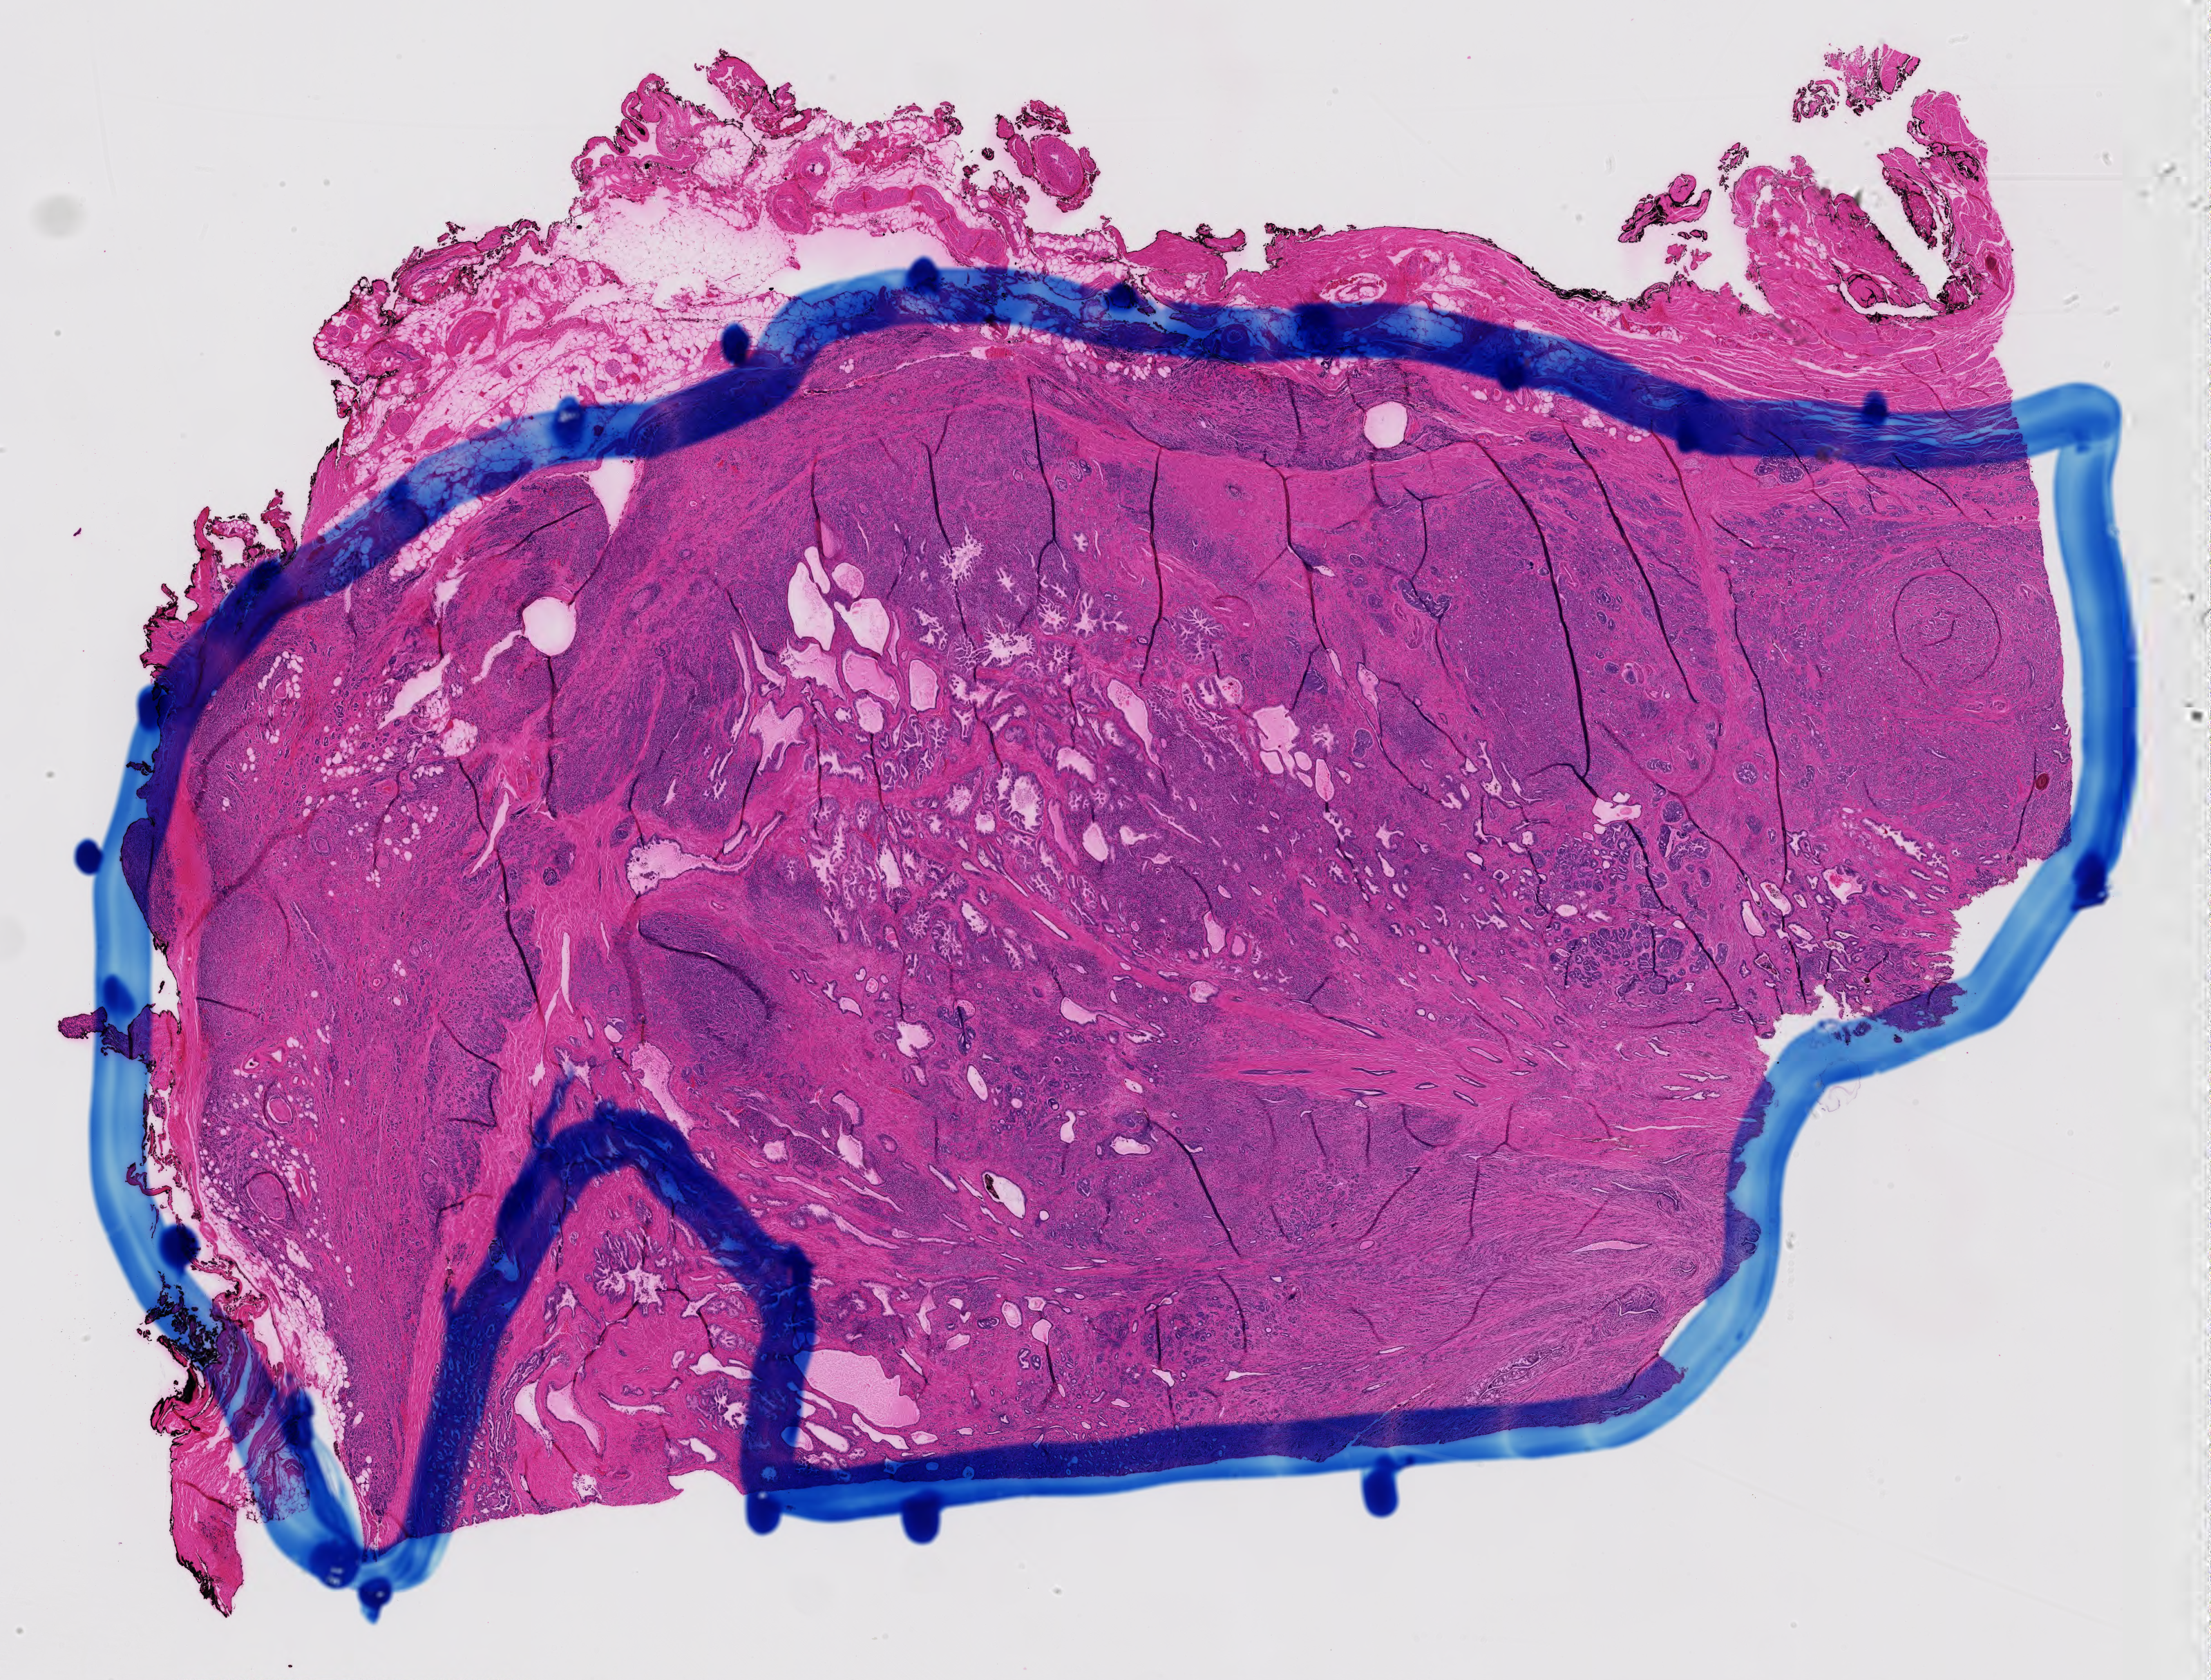
Hematoxylin and eosin (H&E) stained whole-slide image — shown as a low-resolution overview of the whole scanned area (about 23.2 x 17.6 mm), FFPE section, sample: primary tumour, prostate. Male patient; age at initial diagnosis 67 years. Gleason score: 9 (4+5).
Histologic diagnosis: Adenocarcinoma, NOS (prostate gland). Laterality: bilateral.